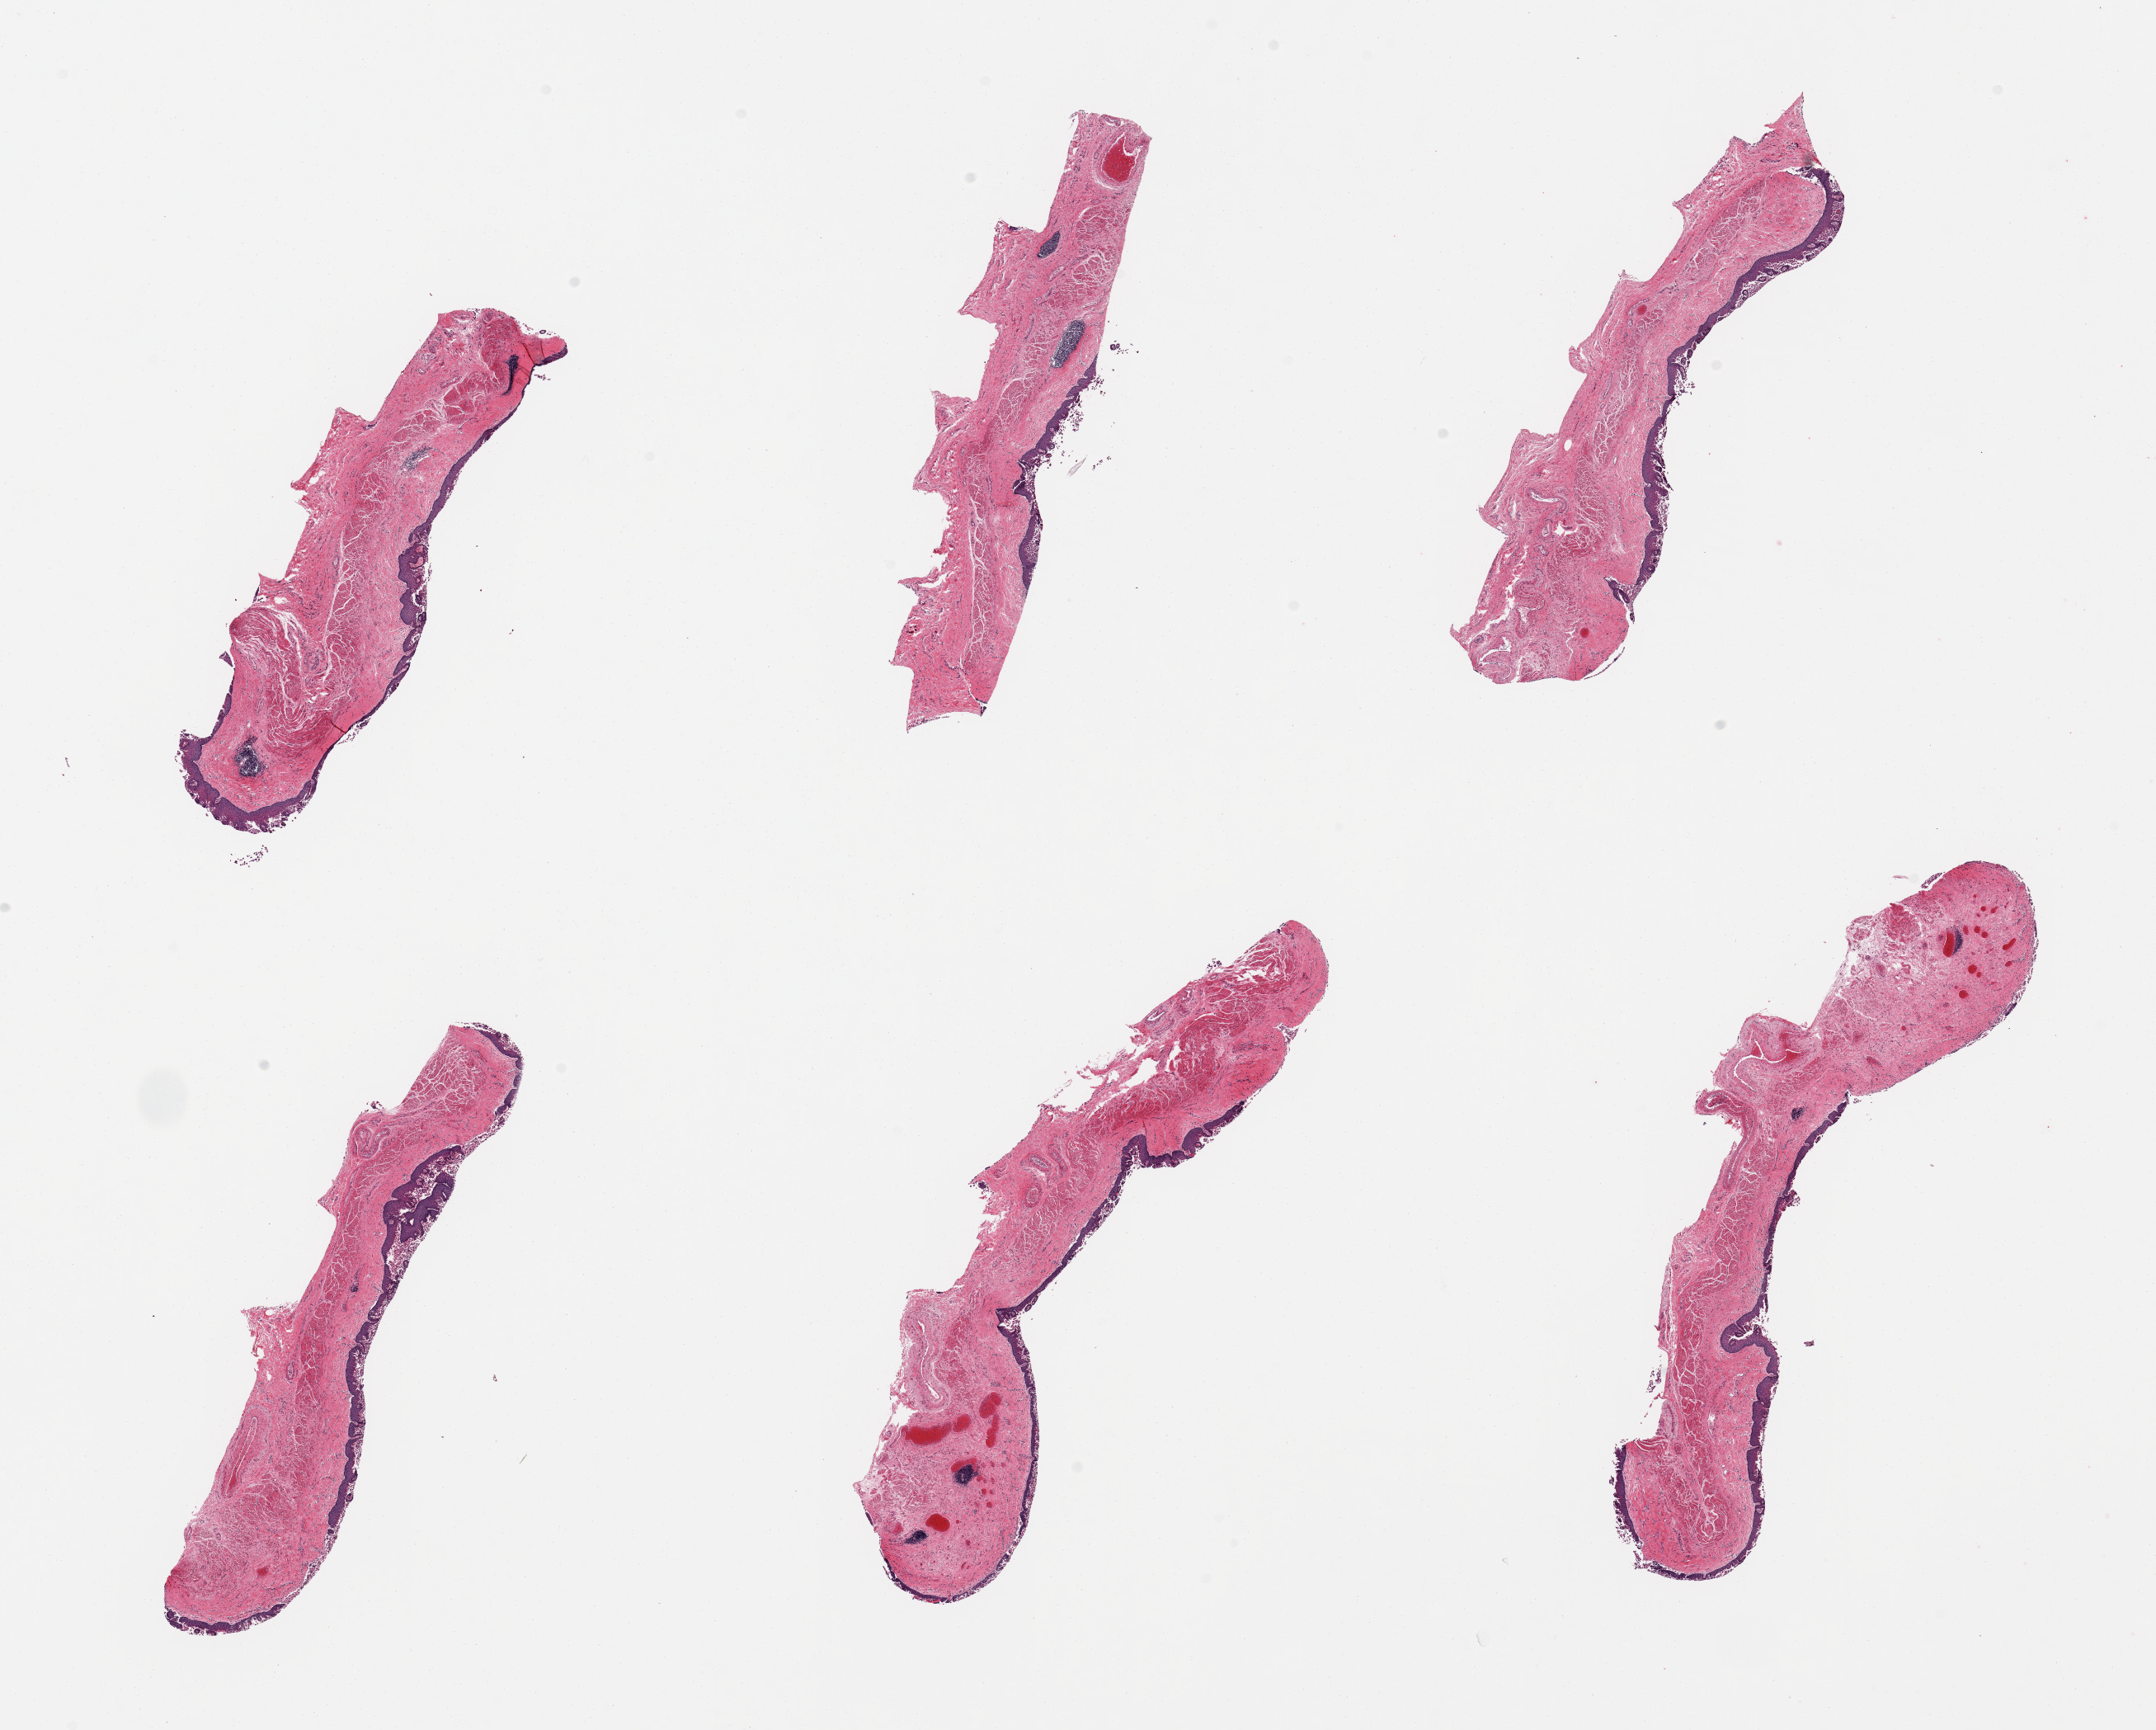
Digitized H&E-stained section, brightfield — whole scanned area (about 20.7 x 16.6 mm, acquisition: 20x scan) shown as a low-resolution overview, PAXgene-fixed, paraffin-embedded tissue, section of esophageal mucous membrane (target tissue), donor tissue sample. Donor sex: male.
• pathologist's review note for this sample: 6 pieces, unusually poorly preserved, target squamous mucosa sloughing, ~0.15mm where visible, chronically inflamed